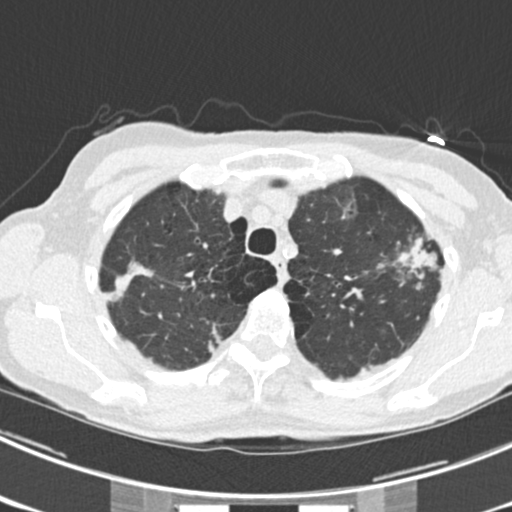
Axial slice from a low-dose chest CT screening exam, third screening round (two years after baseline), lung window (W 1500 / L -600 HU), 512 × 512 image matrix, field of view 302 × 302 mm. Female, age 63 years at enrolment.
Expert reader's lesion annotation, bounding box <376,227,447,288> (left, top, right, bottom; pixels). The screening reader recorded 9 non-calcified nodules or masses ≥4 mm on this exam (left upper lobe, right upper lobe, left upper lobe, left lower lobe, right middle lobe, left lower lobe, left lower lobe, right lower lobe, right lower lobe); which of them this box marks is not recorded. Later outcome: lung cancer diagnosed 15 days after this screen — bronchiolo-alveolar adenocarcinoma, NOS, right upper lobe, right middle lobe, right lower lobe, left upper lobe, left lower lobe, moderately differentiated (G2), stage IV (AJCC 6th edition).